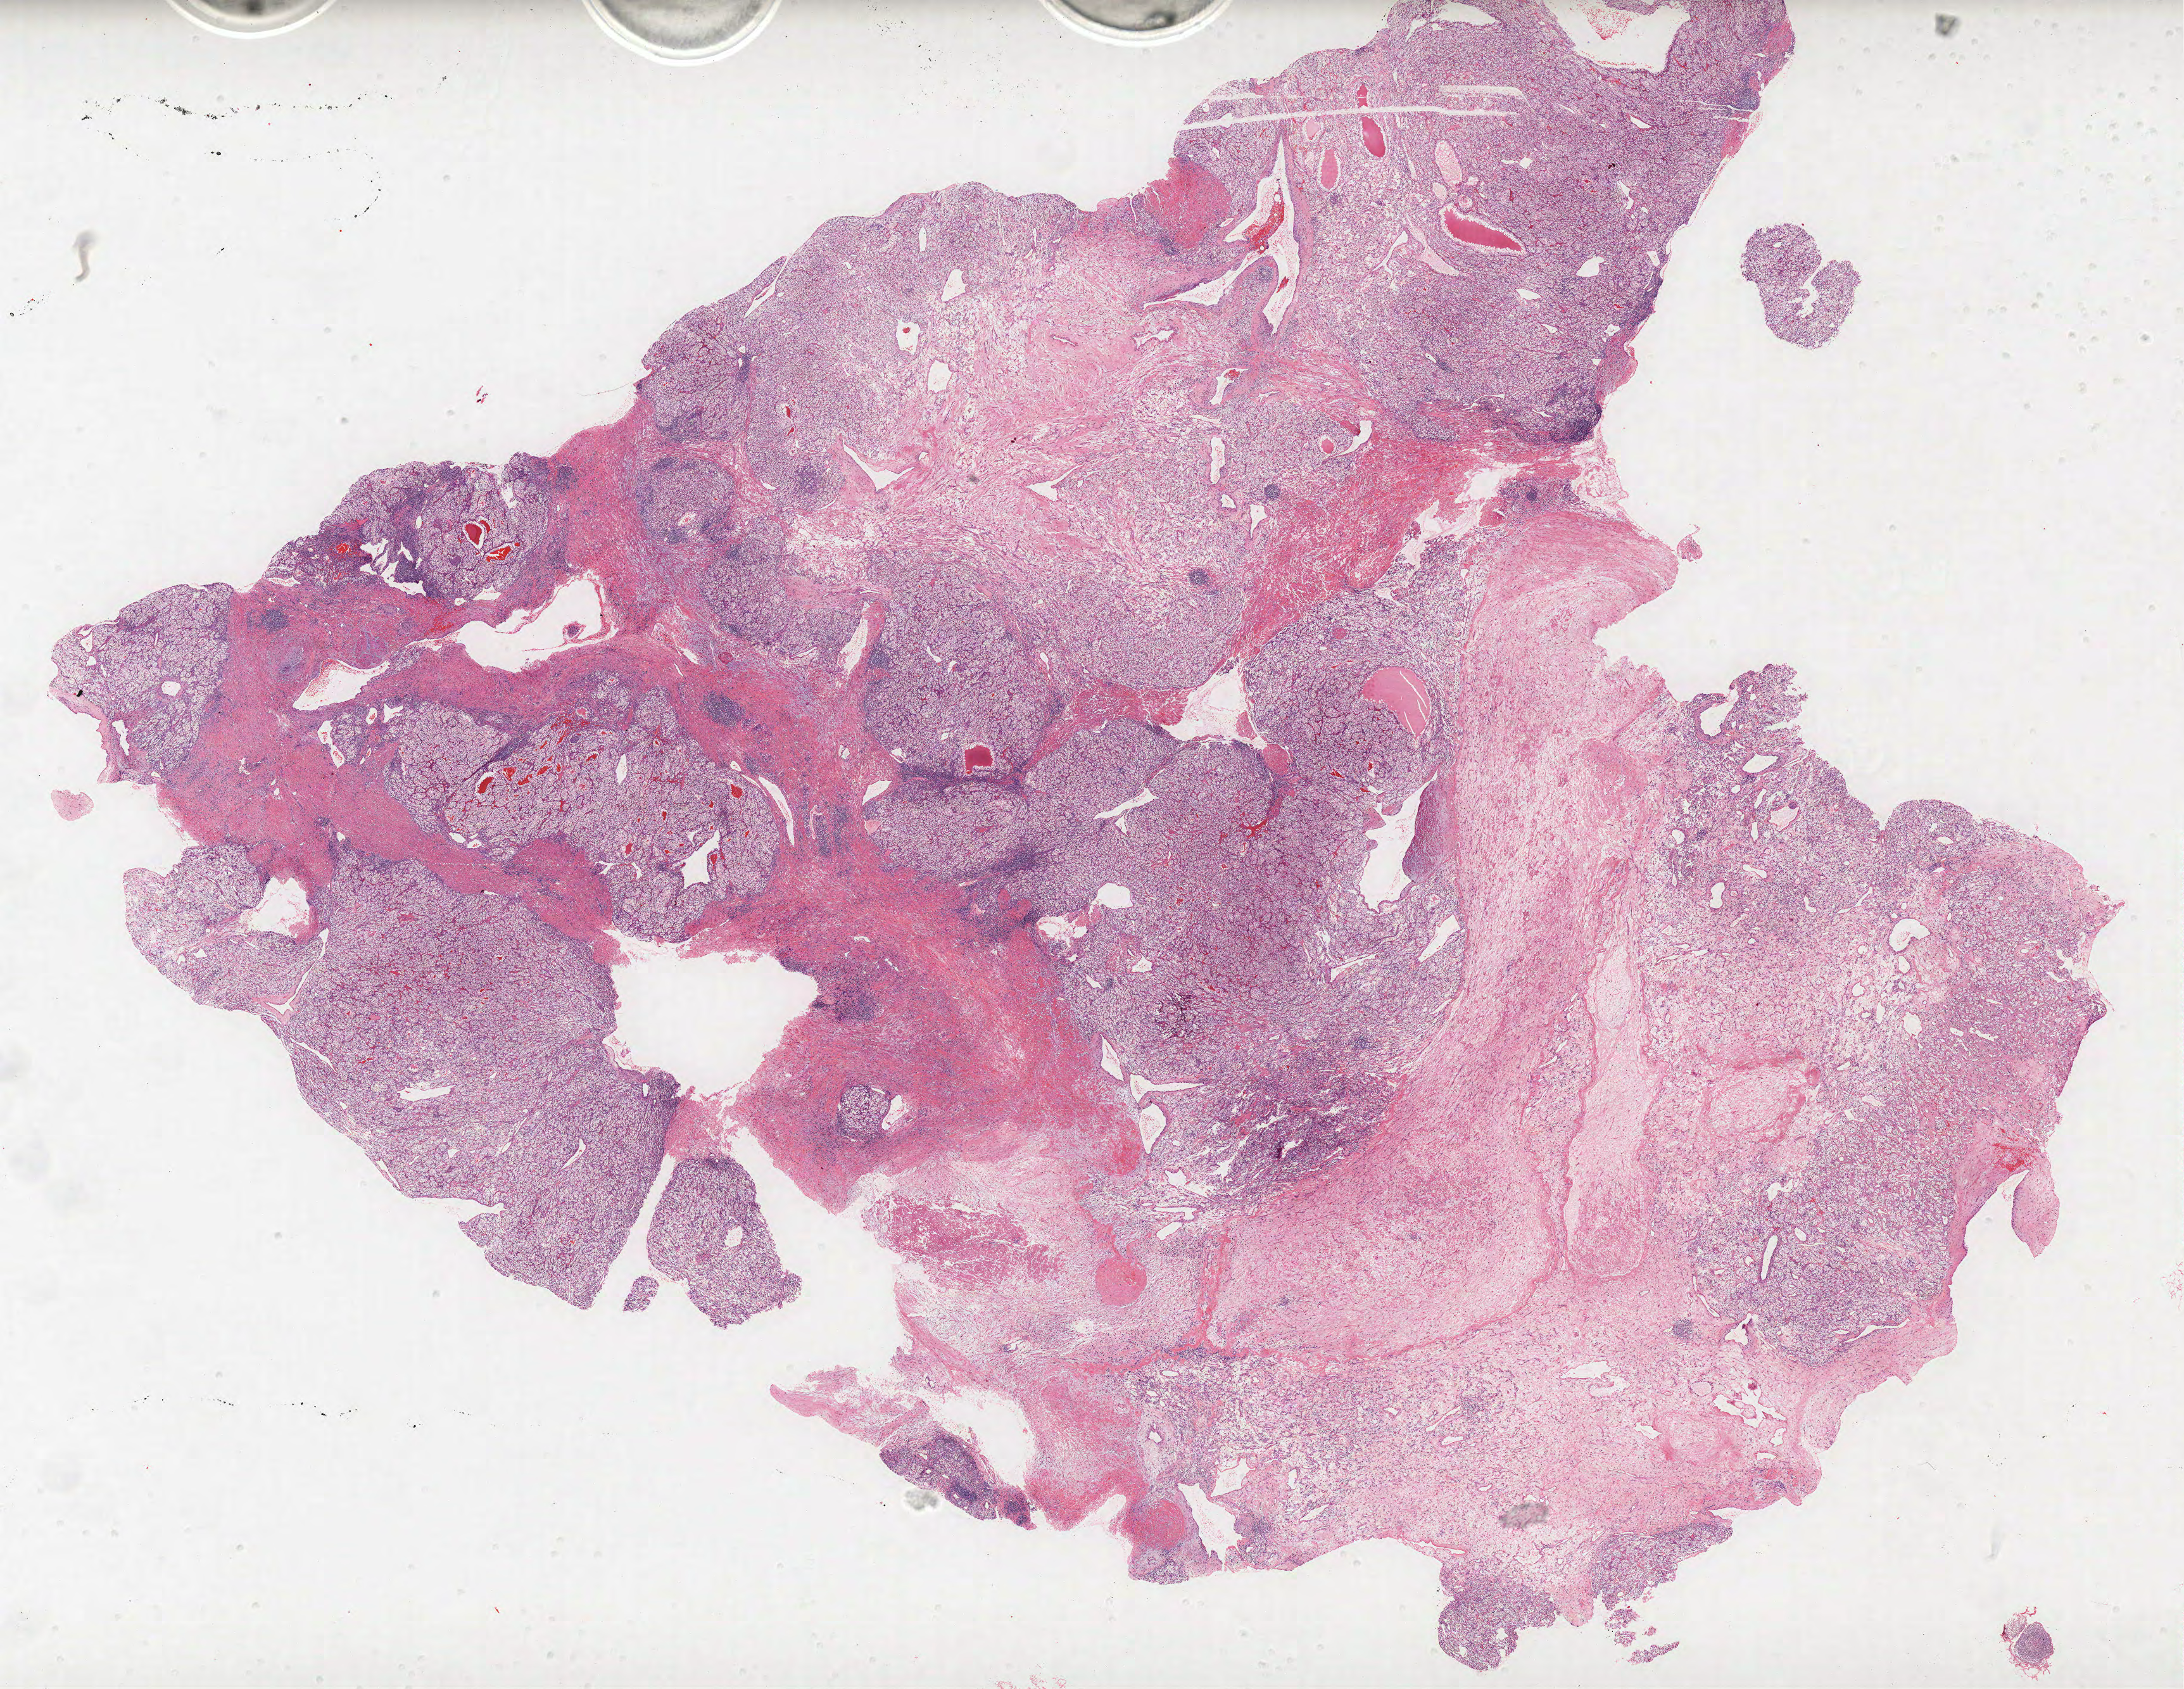
Hematoxylin and eosin (H&E) stained whole-slide image — whole scanned area (about 27.6 x 21.3 mm, from a 40x scan) shown as a low-resolution overview; formalin-fixed paraffin-embedded (FFPE) diagnostic section; sample: primary tumour, kidney. Female patient; age at initial diagnosis 60 years. Histologic grade: G2 (moderately differentiated).
Diagnosis: Clear cell adenocarcinoma, NOS. AJCC pathologic stage: III.